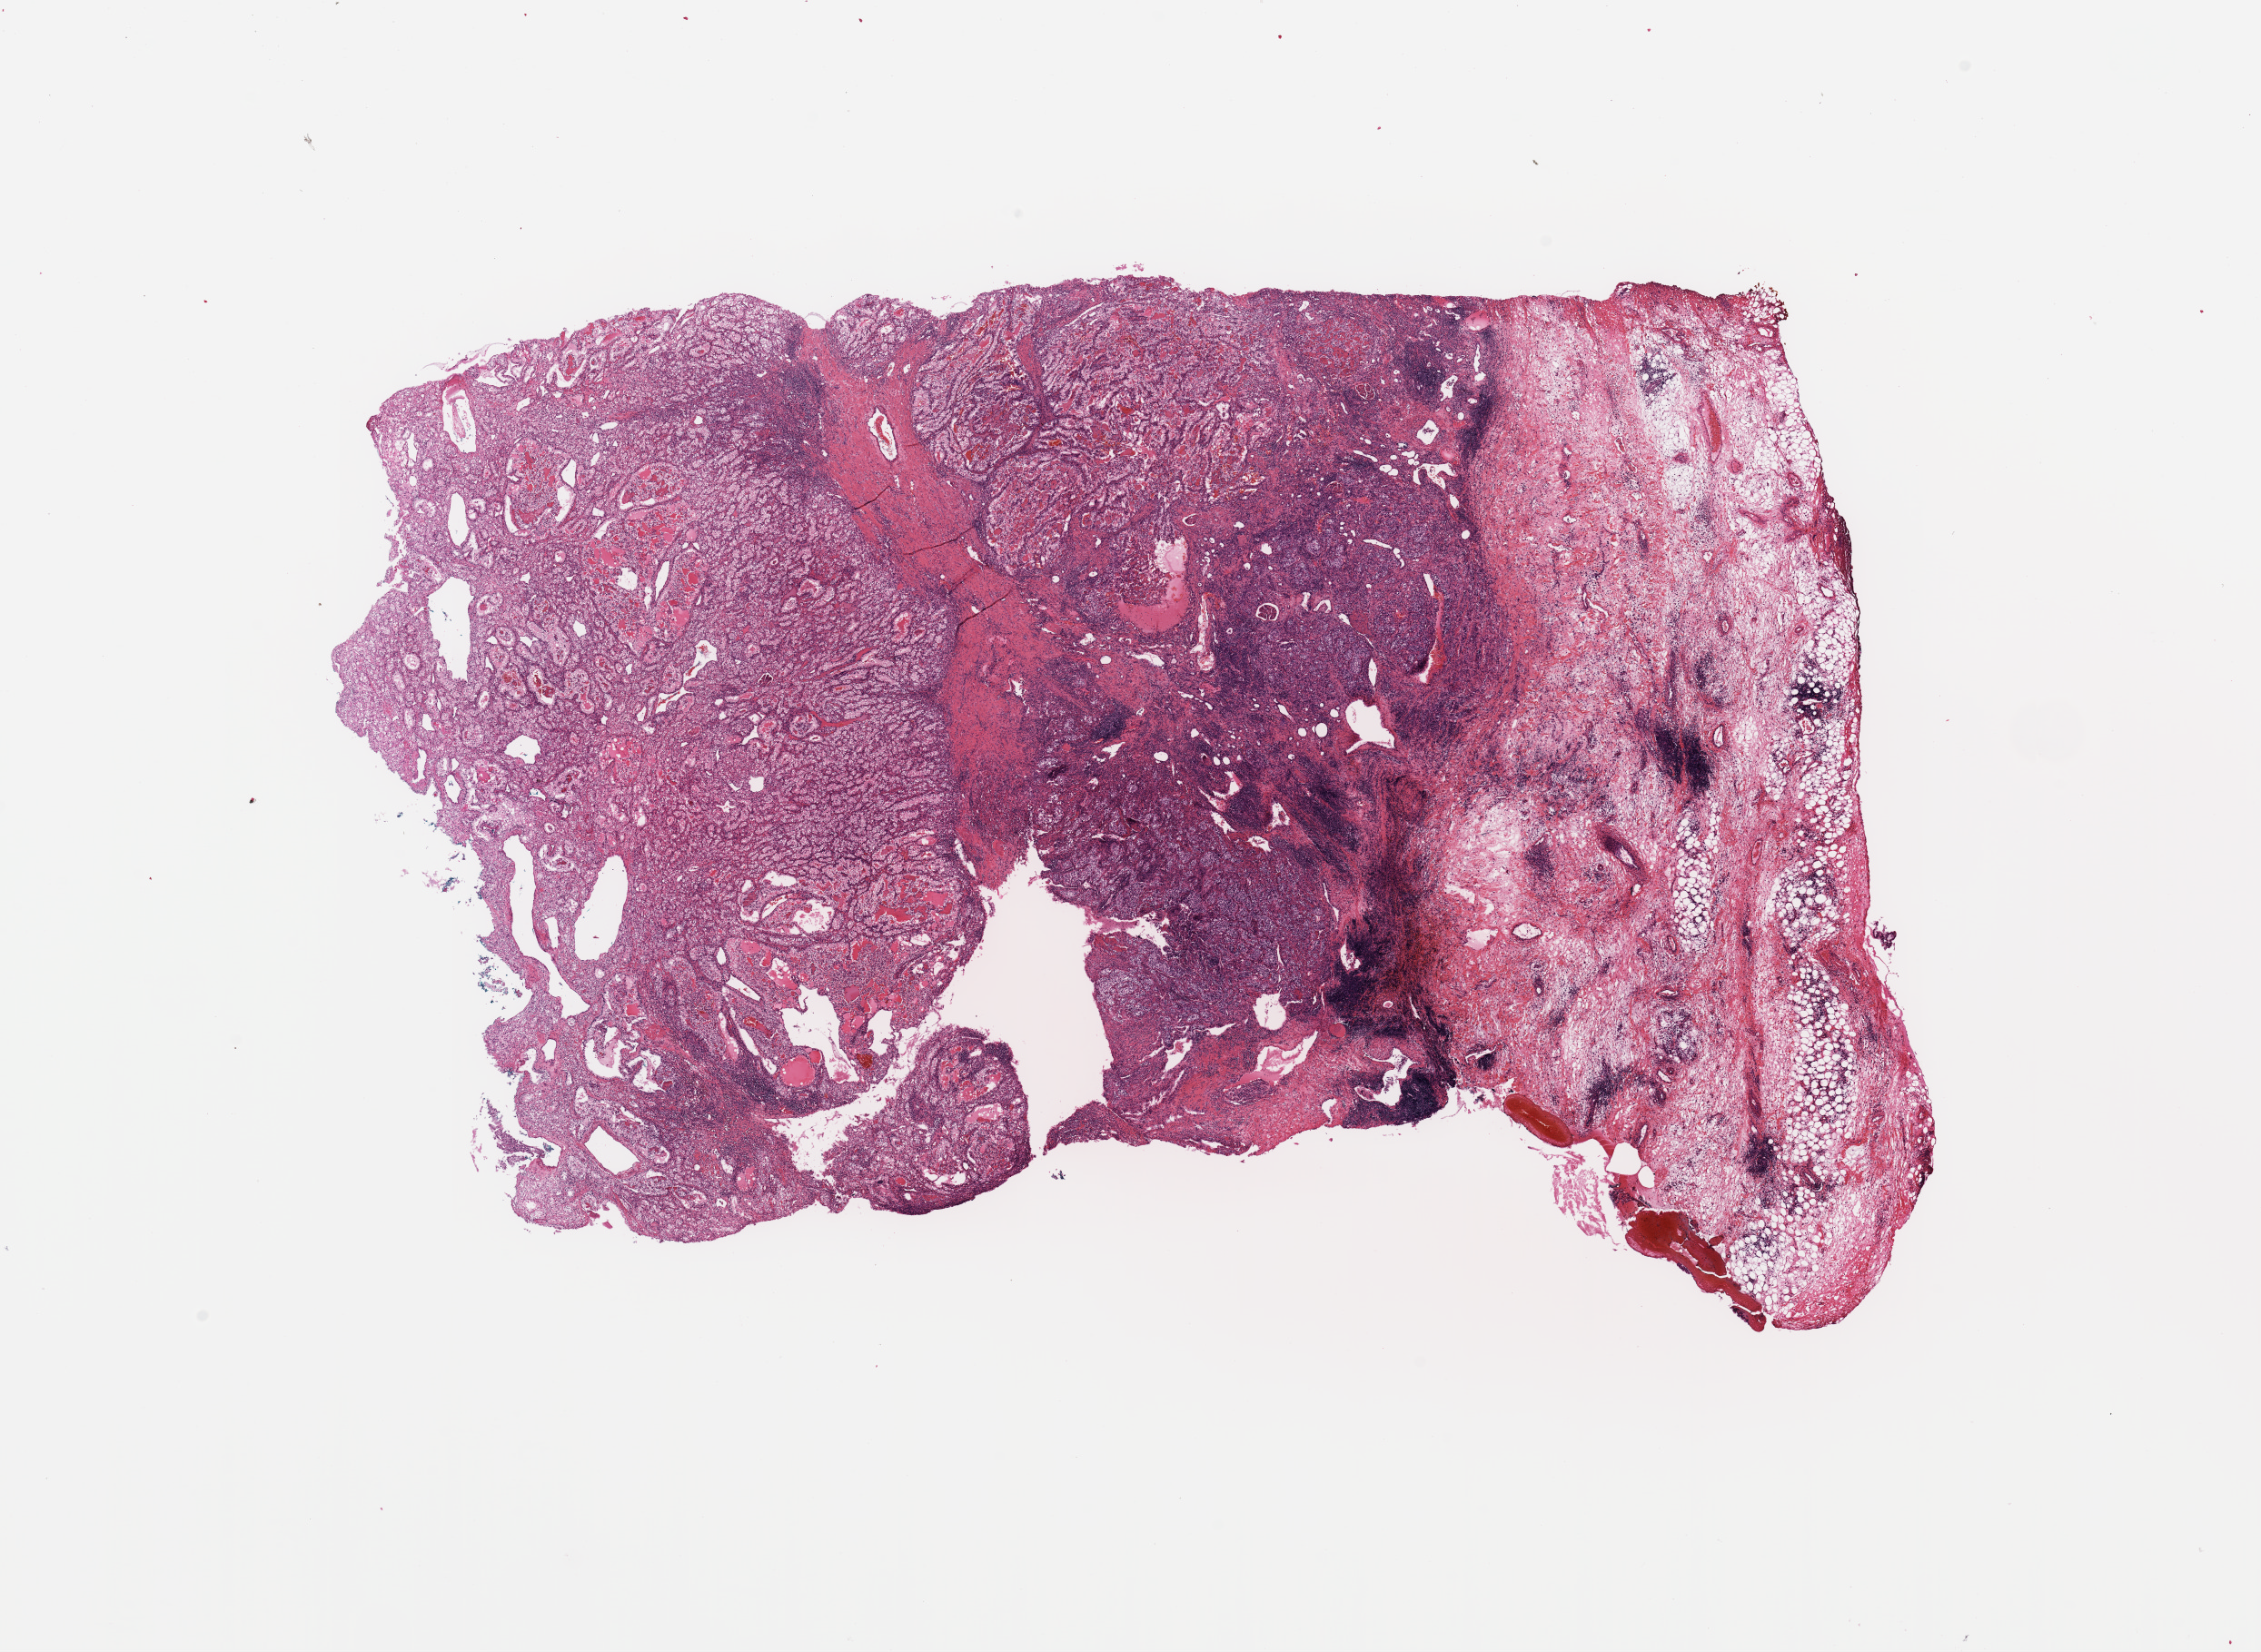
Digitized H&E tissue section (whole slide) — low-resolution overview of the scanned area, about 19.7 x 14.4 mm (slide scanned at 20x). Tumour tissue sample, sampled site: kidney. Patient: male, age 54 years. Histologic grade: G2 (moderately differentiated). Composition of this section per pathologist review: tumour nuclei 85%, necrosis 2%.
• AJCC pathologic stage: II
• diagnosis: Renal cell carcinoma, NOS
• primary tumour site (as recorded): upper pole